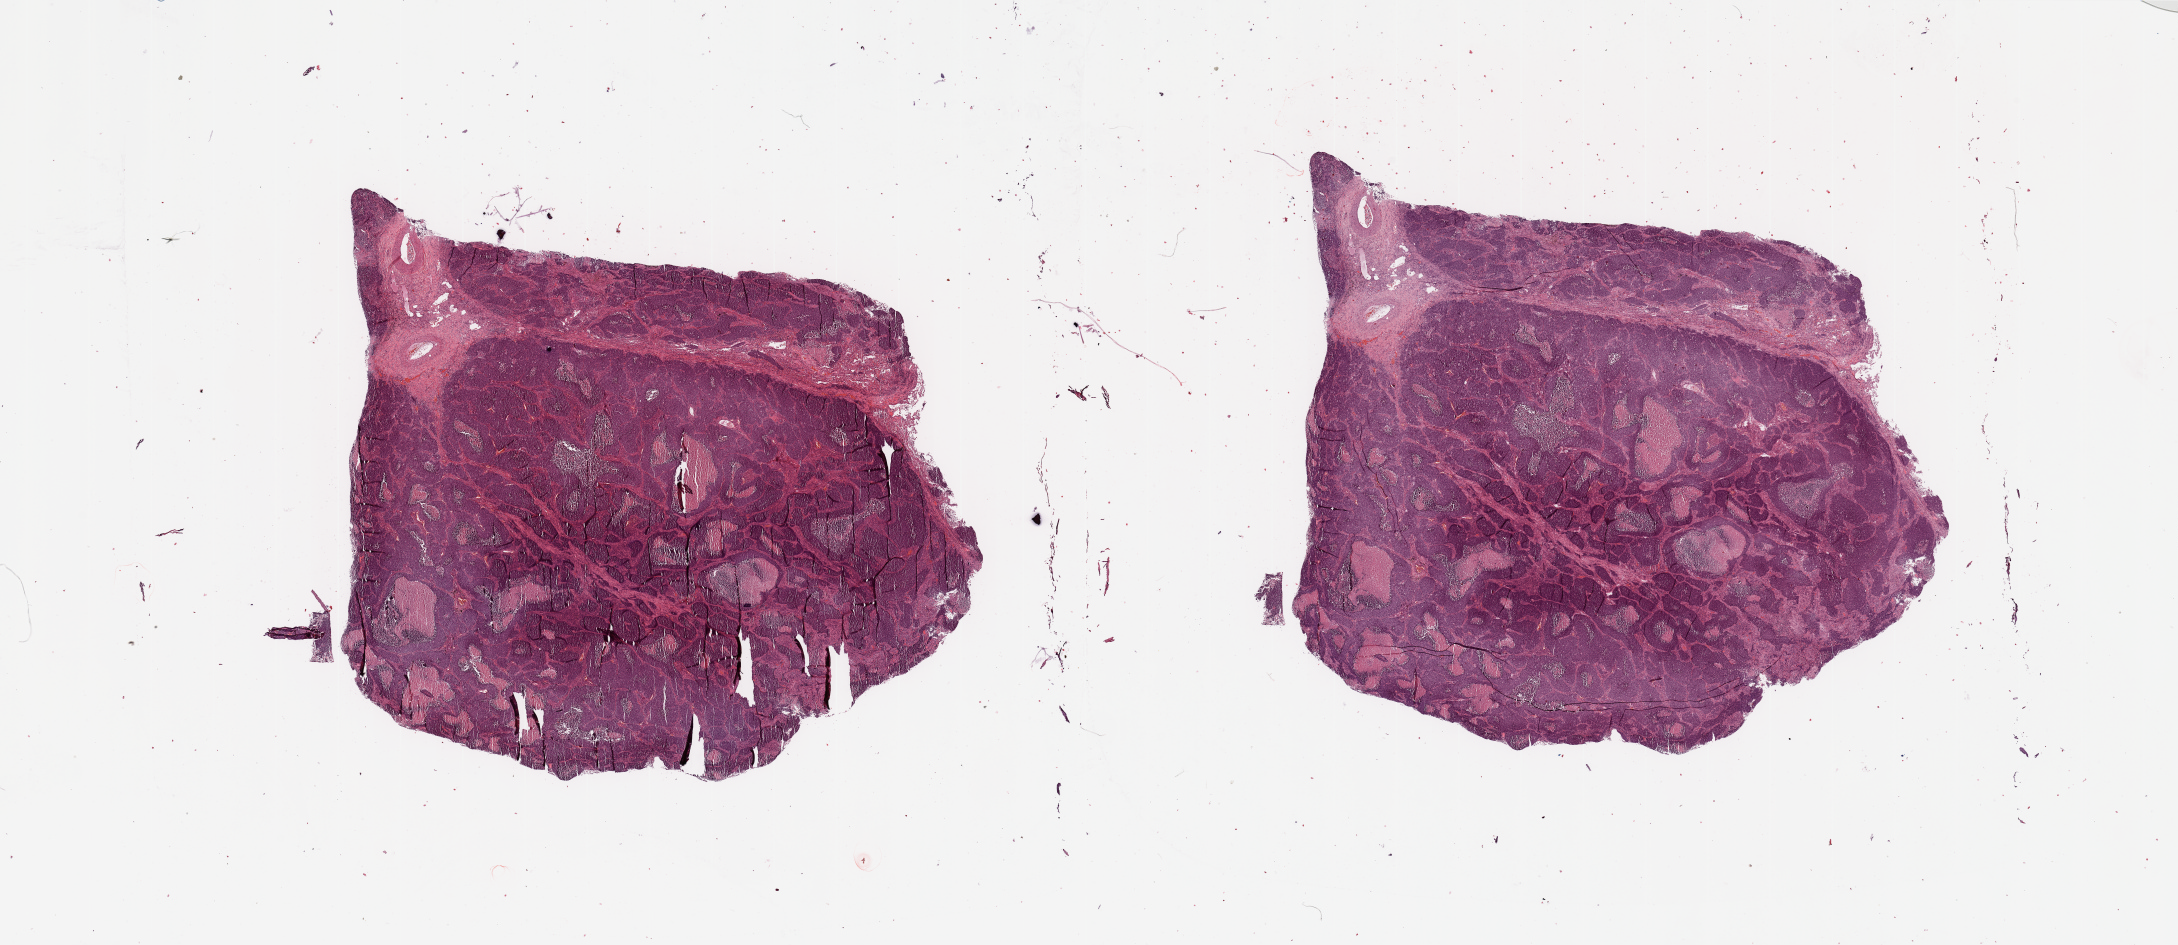
Whole-slide histology image, H&E-stained — a low-resolution overview of the entire scanned area, about 34.5 x 14.9 mm (from a 20x scan), tumour tissue sample, lung. 61-year-old male patient. Histologic grade: G3 (poorly differentiated).
Histologic diagnosis: Squamous cell carcinoma, NOS. AJCC pathologic stage: IIB.